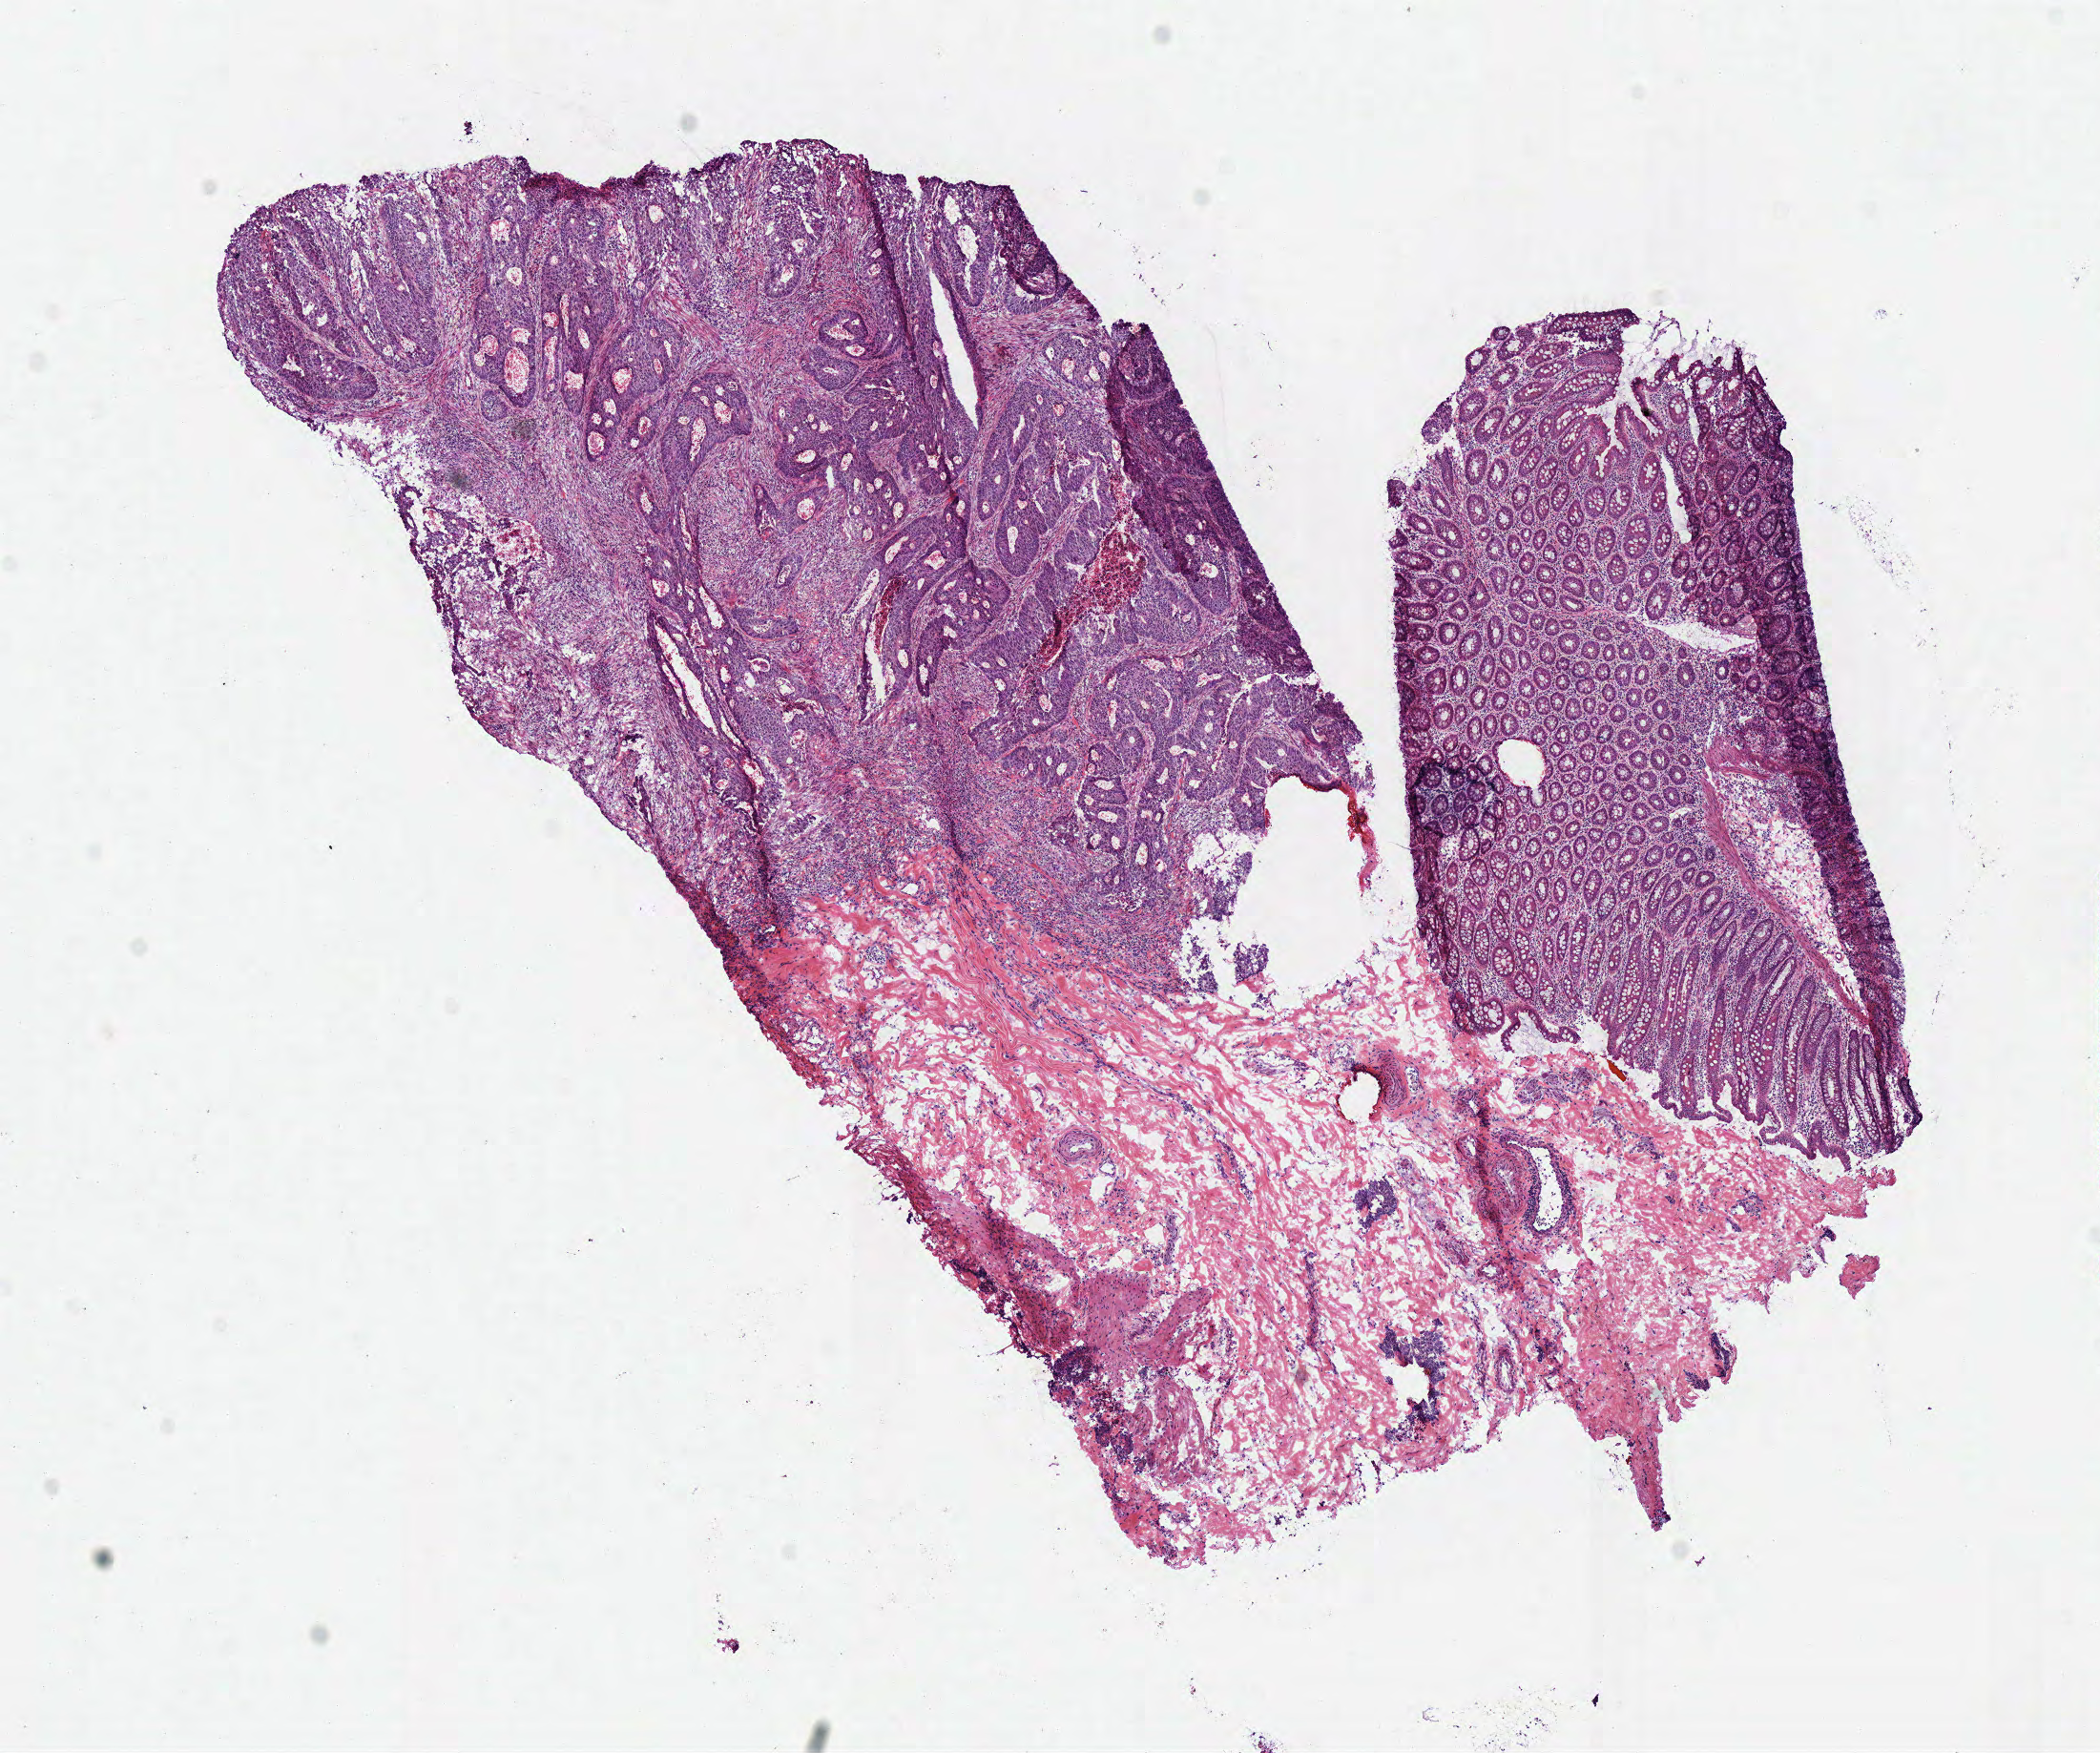
Whole-slide histology image, H&E, low-resolution overview of the scanned area, about 8.7 x 7.2 mm, frozen section from the top of the tissue portion, colon, primary tumour sample. Patient: male, age at initial diagnosis 65 years. Slide review estimates, as recorded: tumour cells 82%, tumour nuclei 80%, normal cells 0%, stromal cells 10%, necrosis 8%. Infiltration values recorded for this section: lymphocyte infiltration 10%.
• diagnosis: Adenocarcinoma, NOS (ascending colon)
• lymph nodes positive (case pathology): 0 of 22 examined